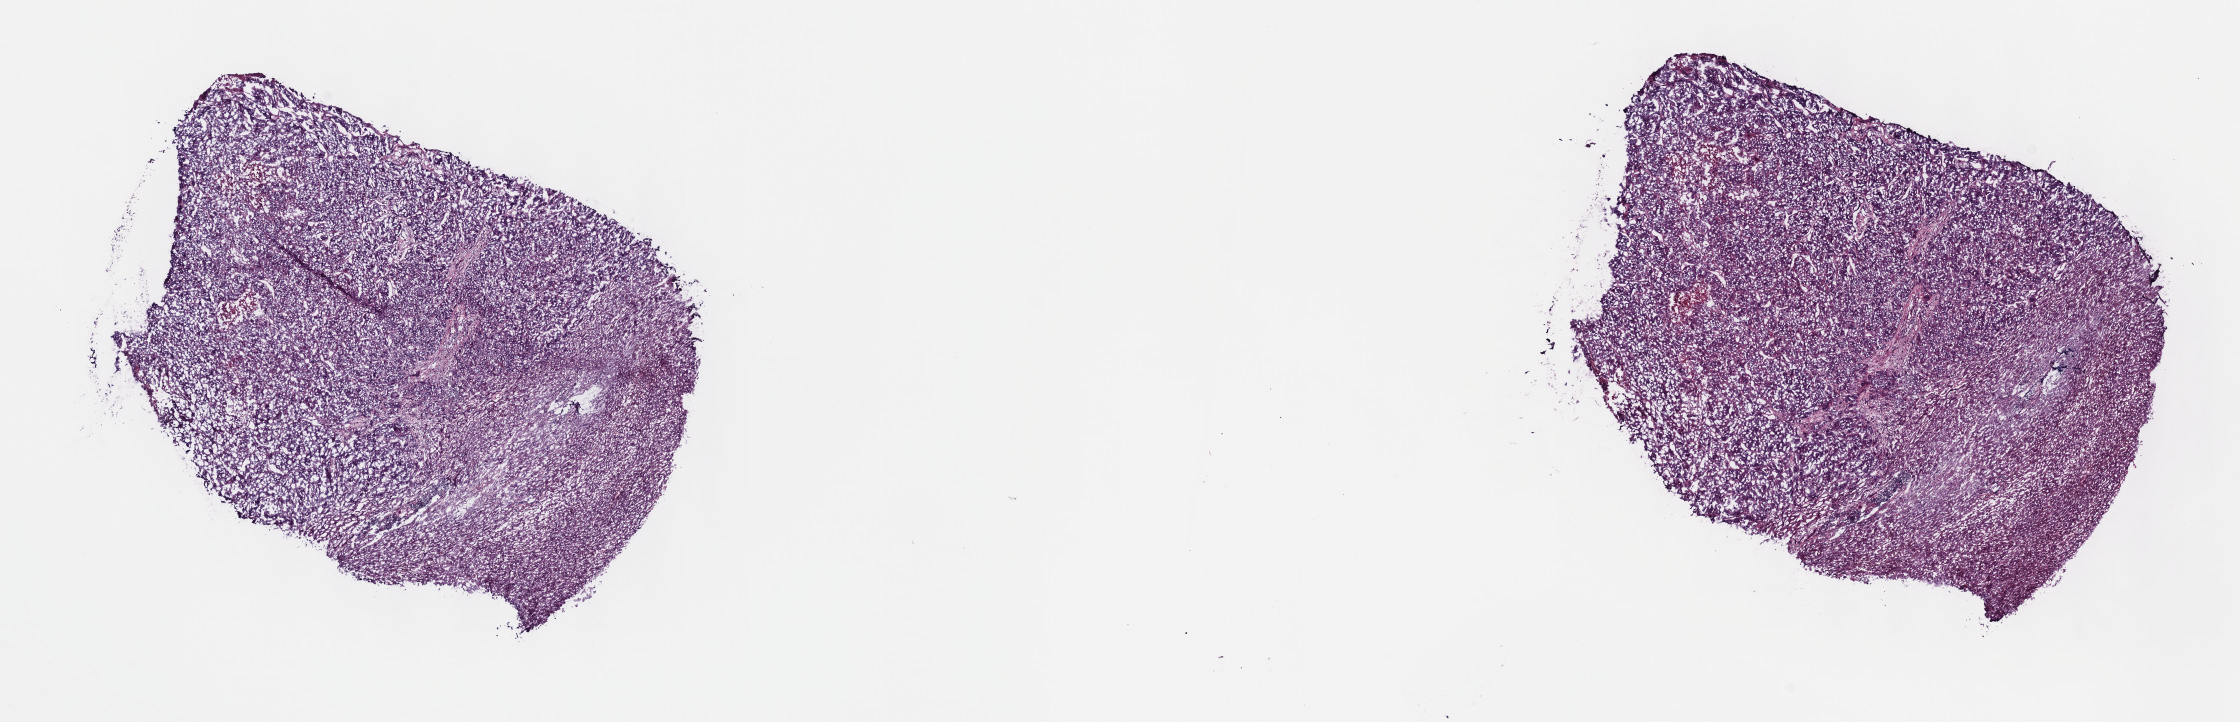
Digitized Hematoxylin and eosin (H&E) stained tissue section (whole slide), shown as a low-resolution overview of the whole scanned area (about 18.1 x 5.8 mm, acquisition: 40x scan); frozen section; primary tumour sample from the liver. Female patient; age at initial diagnosis 71 years. Histologic grade: G3 (poorly differentiated). Composition of this section per pathologist review: tumour cells 100%, tumour nuclei 75%, normal cells 0%, stromal cells 0%, necrosis 0%. Infiltration values recorded for this section: lymphocyte infiltration 3%, monocyte infiltration 0%, neutrophil infiltration 0%.
Pathologic diagnosis: Hepatocellular carcinoma, NOS.